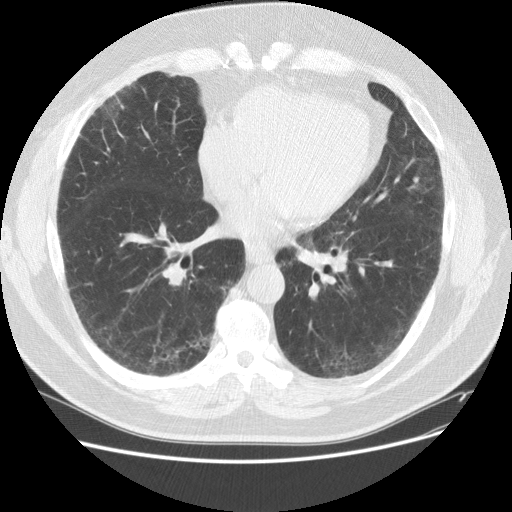
Chest CT (low-dose screening protocol), one axial image; first (baseline) screen; lung window (W 1500 / L -600 HU); 2.5 mm slice thickness; standard (soft-tissue) reconstruction kernel (STANDARD); slice 81 of 151 in the series. Male participant, aged 59 years at enrolment. Current smoker at enrolment.
Expert-annotated lung lesion, box from (x=85, y=85) to (x=130, y=137) px. The screening reader recorded 2 non-calcified nodules or masses ≥4 mm on this exam (right middle lobe, right lower lobe); which of them this box marks is not recorded. Lung cancer was diagnosed 338 days after this screen: adenocarcinoma, NOS, right upper lobe, right middle lobe, moderately differentiated (G2), stage IA (AJCC 6th edition), 13 mm at pathology.